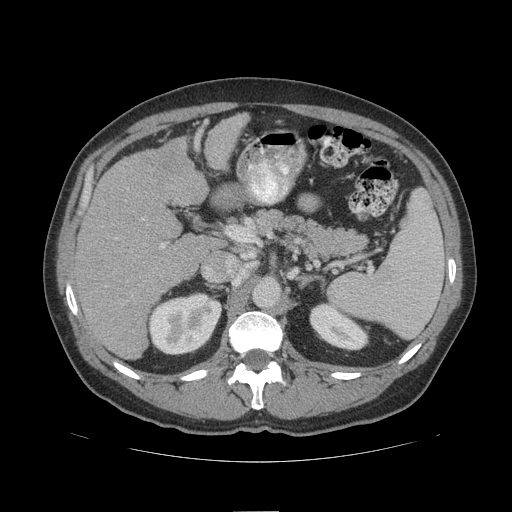
Contrast-enhanced abdominal CT (liver protocol), one axial slice. Slice 60 of 109 in the series (ordered by position). Soft-tissue window (W 400 / L 40 HU). 2.5 mm slice thickness. 512 × 512 image matrix, field of view 420 × 420 mm. From the clinical record (not read from this slice): diagnosis: hepatocellular carcinoma (patient treated with transarterial chemoembolisation; whether this scan precedes or follows treatment is not stated here); TNM stage (as recorded): Stage-IIIB; Child-Pugh class: A.
Annotated regions visible in this slice (semi-automatic segmentation, software-assisted and operator-edited):
- liver parenchyma outside the tumour (the mass and vessels are separate outlines, so this box may not span the whole liver): box from (x=74, y=112) to (x=248, y=360) px
- liver vessels: (x=161, y=244)–(x=164, y=247)